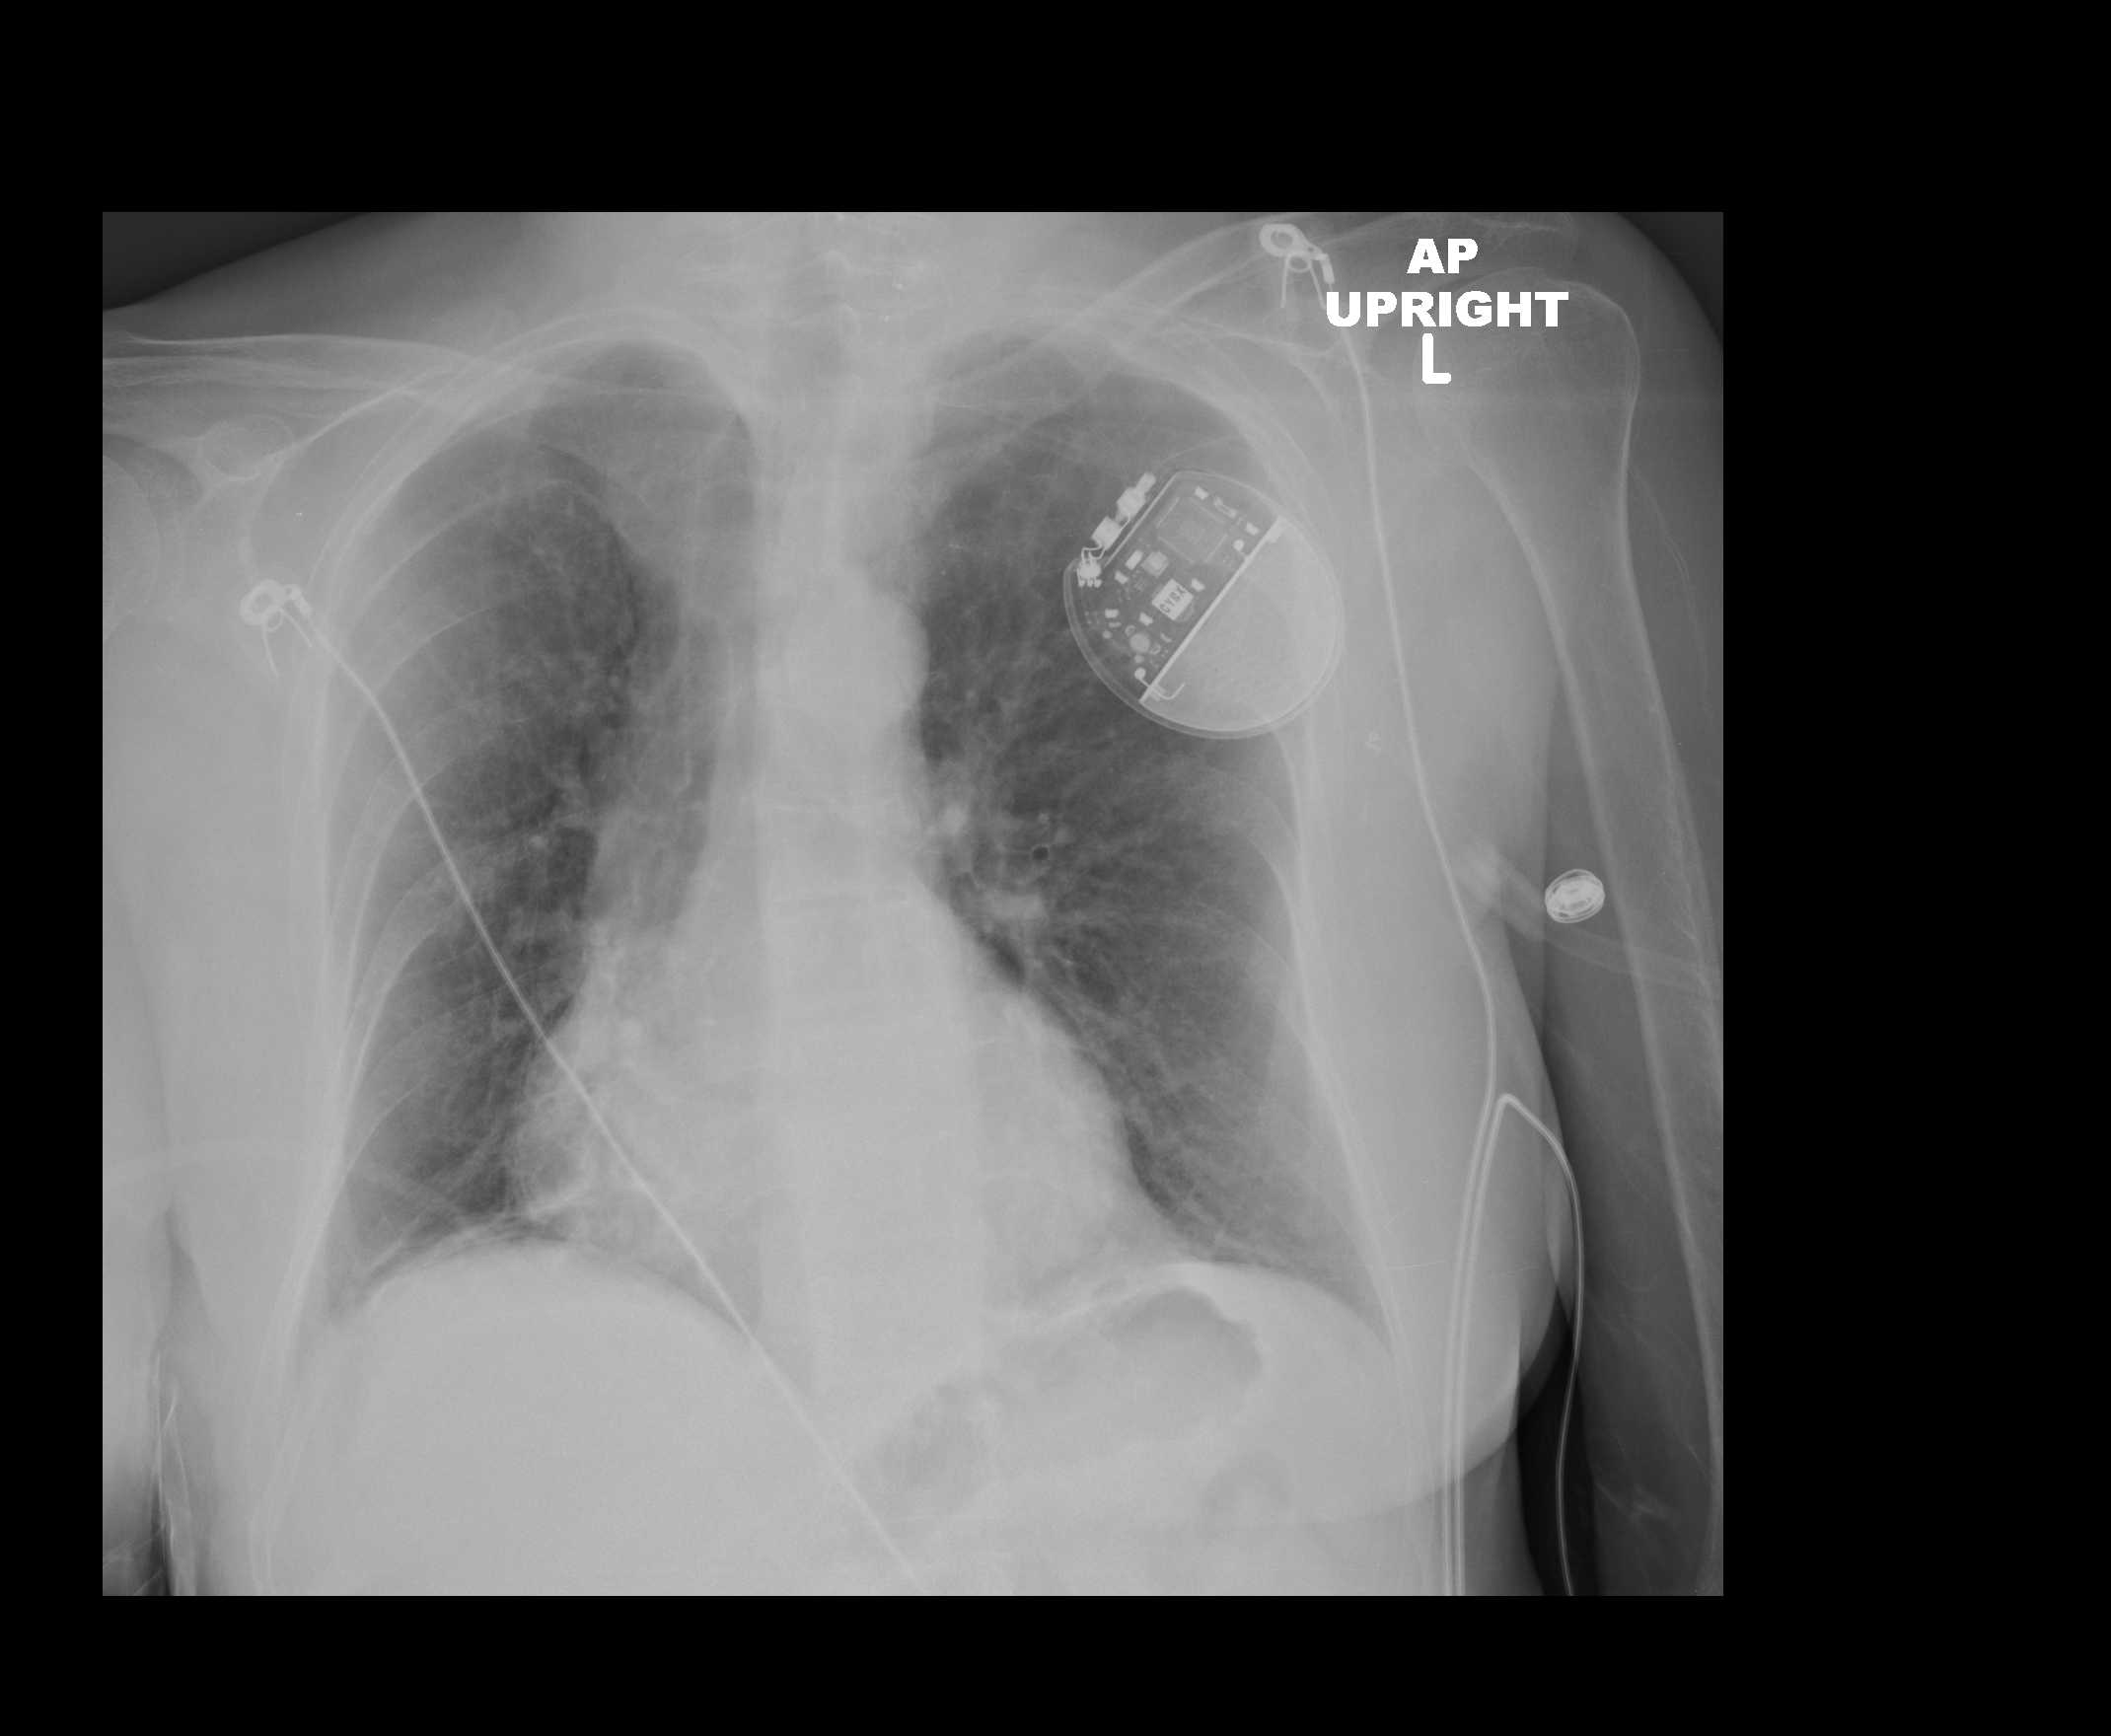
Chest radiograph. Female patient, age 70 years; imaged 0 days after the COVID-19 diagnosis.
Key findings recorded by the radiologist: Lungs are clear, no nodule, airspace disease or pleural effusion.